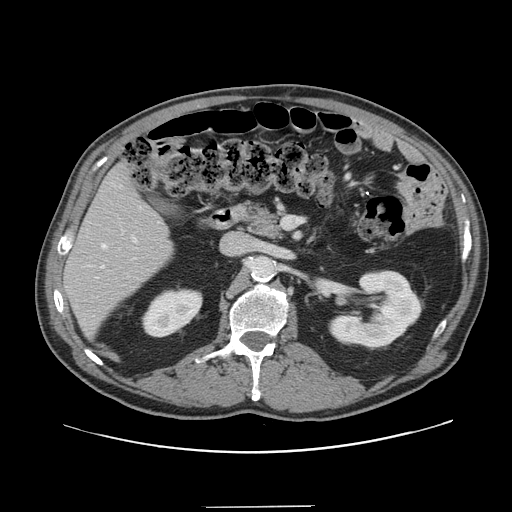
Contrast-enhanced abdominal CT, one axial slice. Position 70 of 139 along the scan axis. Intravenous contrast given. Soft-tissue window (W 400 / L 40 HU). 2.5 mm slice thickness. 512 × 512 image matrix. Male patient, age 64 years. Case-level facts recorded for this patient, not image findings: diagnosis: colorectal cancer liver metastases, imaged before liver resection; multiple liver metastases: yes; largest metastasis: 3.5 cm; chemotherapy before resection: yes.
Annotated regions visible in this slice (manually delineated by an expert):
- hepatic veins: bounding box (x1, y1, x2, y2) in pixels: (101, 244, 106, 268)
- liver: (65, 167, 172, 334)
- planned liver remnant (the part of the liver to remain after resection): (65, 168, 171, 334)
- portal vein (with intrahepatic branches): (132, 236, 137, 242)